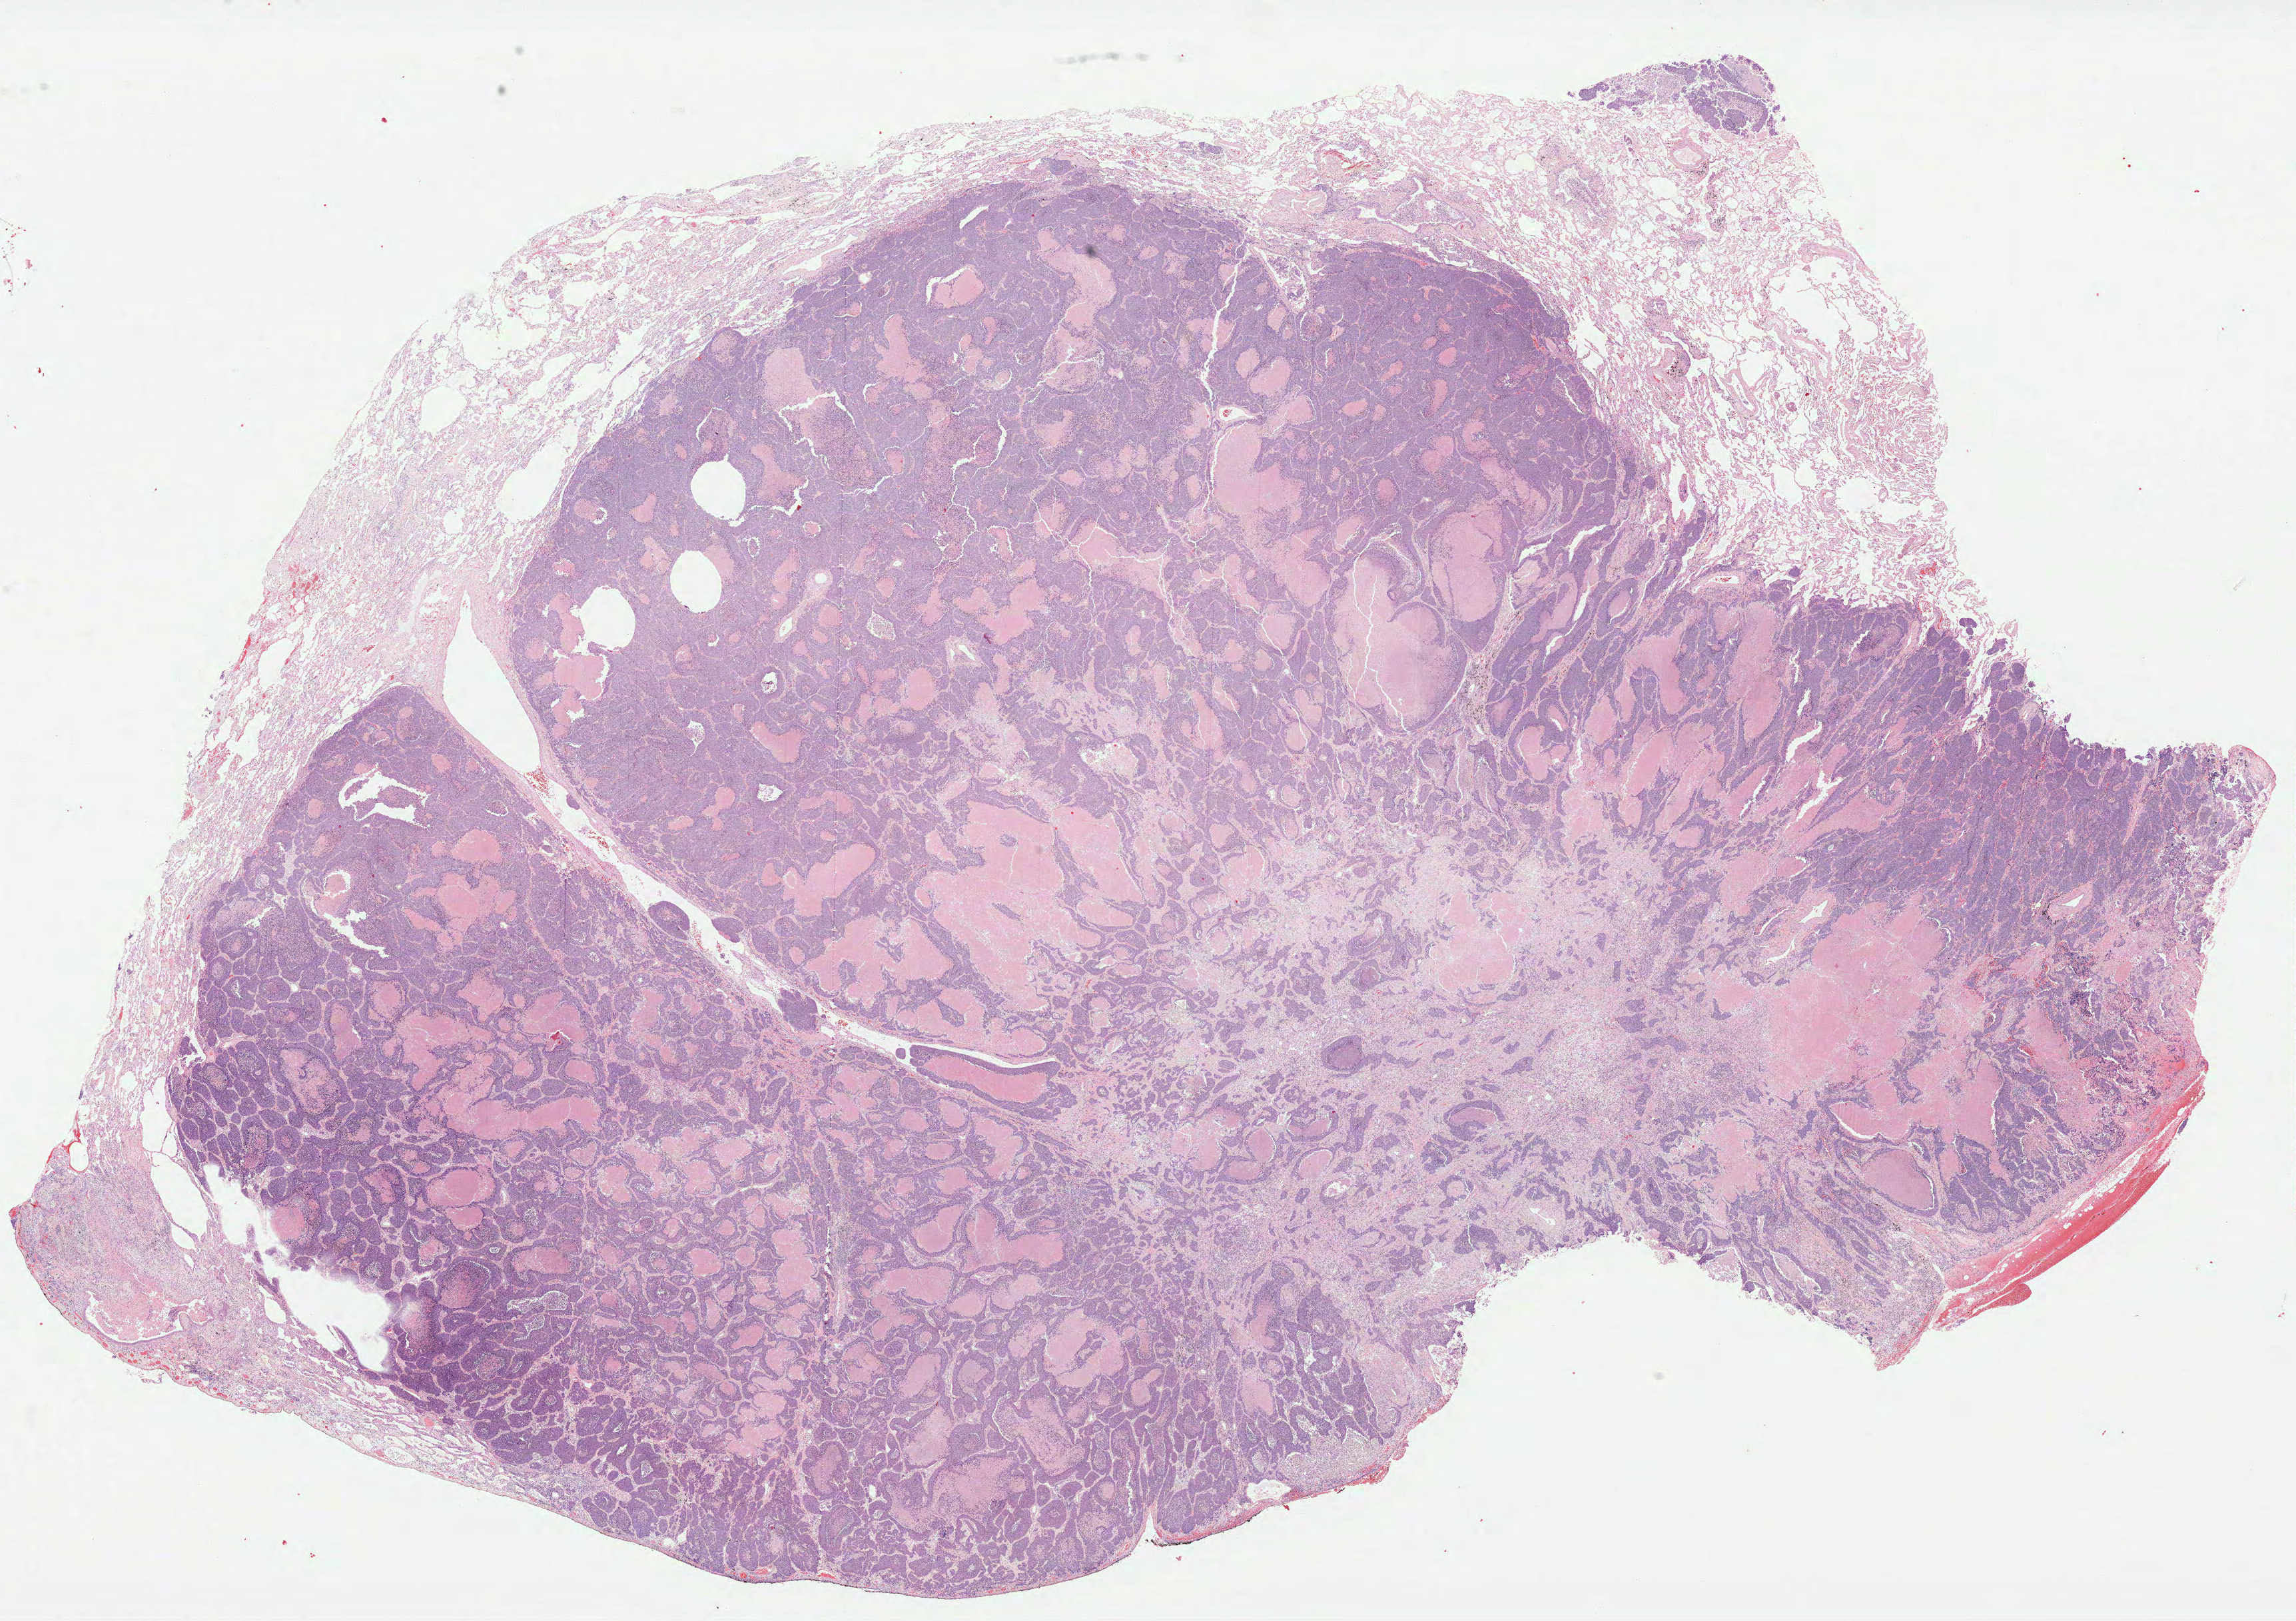
Digitized H&E tissue section (whole slide), whole scanned area (about 27.8 x 19.6 mm) shown as a low-resolution overview. Formalin-fixed paraffin-embedded (FFPE) diagnostic section. Sample: primary tumour, lung. Female patient; age at initial diagnosis 74 years.
Pathologic diagnosis: Basaloid squamous cell carcinoma.